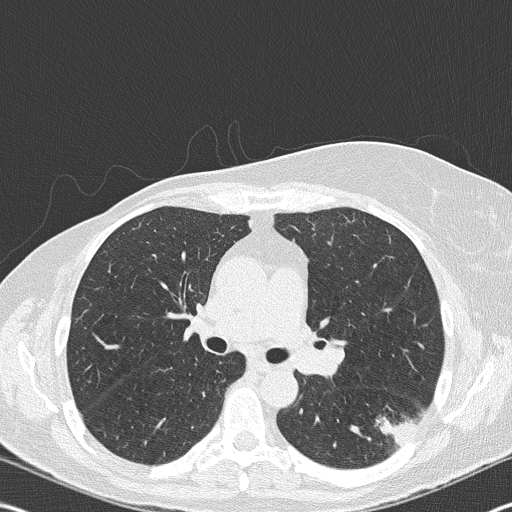
Chest CT (low-dose screening protocol), one axial image; second annual screen; lung window (W 1500 / L -600 HU). Female participant, aged 60 years at enrolment. Current smoker at enrolment.
Lesion marked by an expert reader, bounding box (x1, y1, x2, y2) in pixels: (367, 387, 433, 450). Reader record for this screening exam (exam-level; its link to the box is not recorded): non-calcified nodule or mass ≥4 mm, left lower lobe, 18 × 16 mm, spiculated (stellate) margins, soft tissue attenuation, pre-existing on the prior screen: no. Later outcome: lung cancer diagnosed 35 days after this screen — carcinoma, NOS, left hilum, stage IV (AJCC 6th edition), 45 mm at pathology.